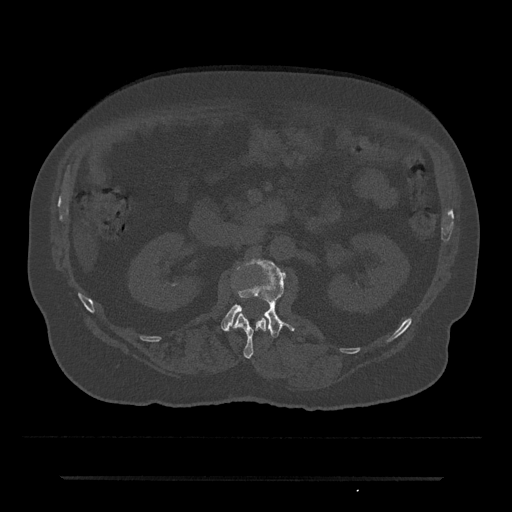
CT including the spine, one axial slice. Position 35 of 797 along the scan axis. Reconstruction kernel Br40s/3. 120 kVp. Bone window (W 1800 / L 400 HU). 0.5 mm slice thickness. 512 × 512 image matrix. Patient: male, 69 years. From the clinical record (not read from this slice): primary cancer: prostate.
Annotated regions visible in this slice (semi-automatic segmentation, software-assisted and operator-edited):
- L1 vertebra: bounding box (x1, y1, x2, y2) in pixels: (233, 313, 267, 358)
- L2 vertebra: (221, 259, 294, 338)